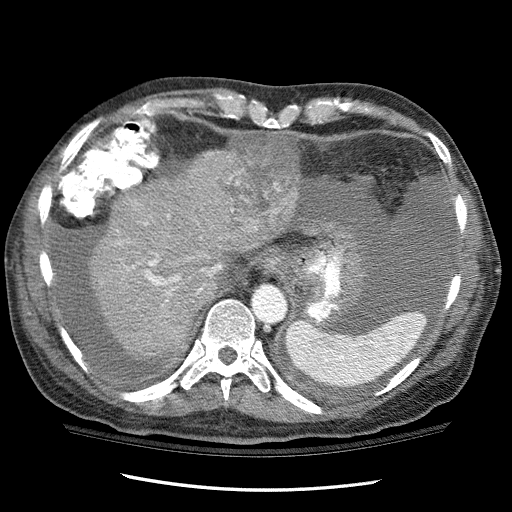
Contrast-enhanced abdominal CT (liver protocol), one axial slice. One of 3 acquisitions stored at this slice position. Soft-tissue window (W 400 / L 40 HU). 512 × 512 image matrix, field of view 360 × 360 mm. Case-level facts recorded for this patient, not image findings: diagnosis: hepatocellular carcinoma (patient treated with transarterial chemoembolisation; whether this scan precedes or follows treatment is not stated here); TNM stage (as recorded): Stage-I.
Structures marked on this image (semi-automatically segmented with operator editing):
- liver parenchyma outside the tumour (the mass and vessels are separate outlines, so this box may not span the whole liver): bounding box (x1, y1, x2, y2) in pixels: (90, 150, 298, 364)
- mass: (177, 134, 299, 252)
- liver vessels: (132, 223, 221, 295)